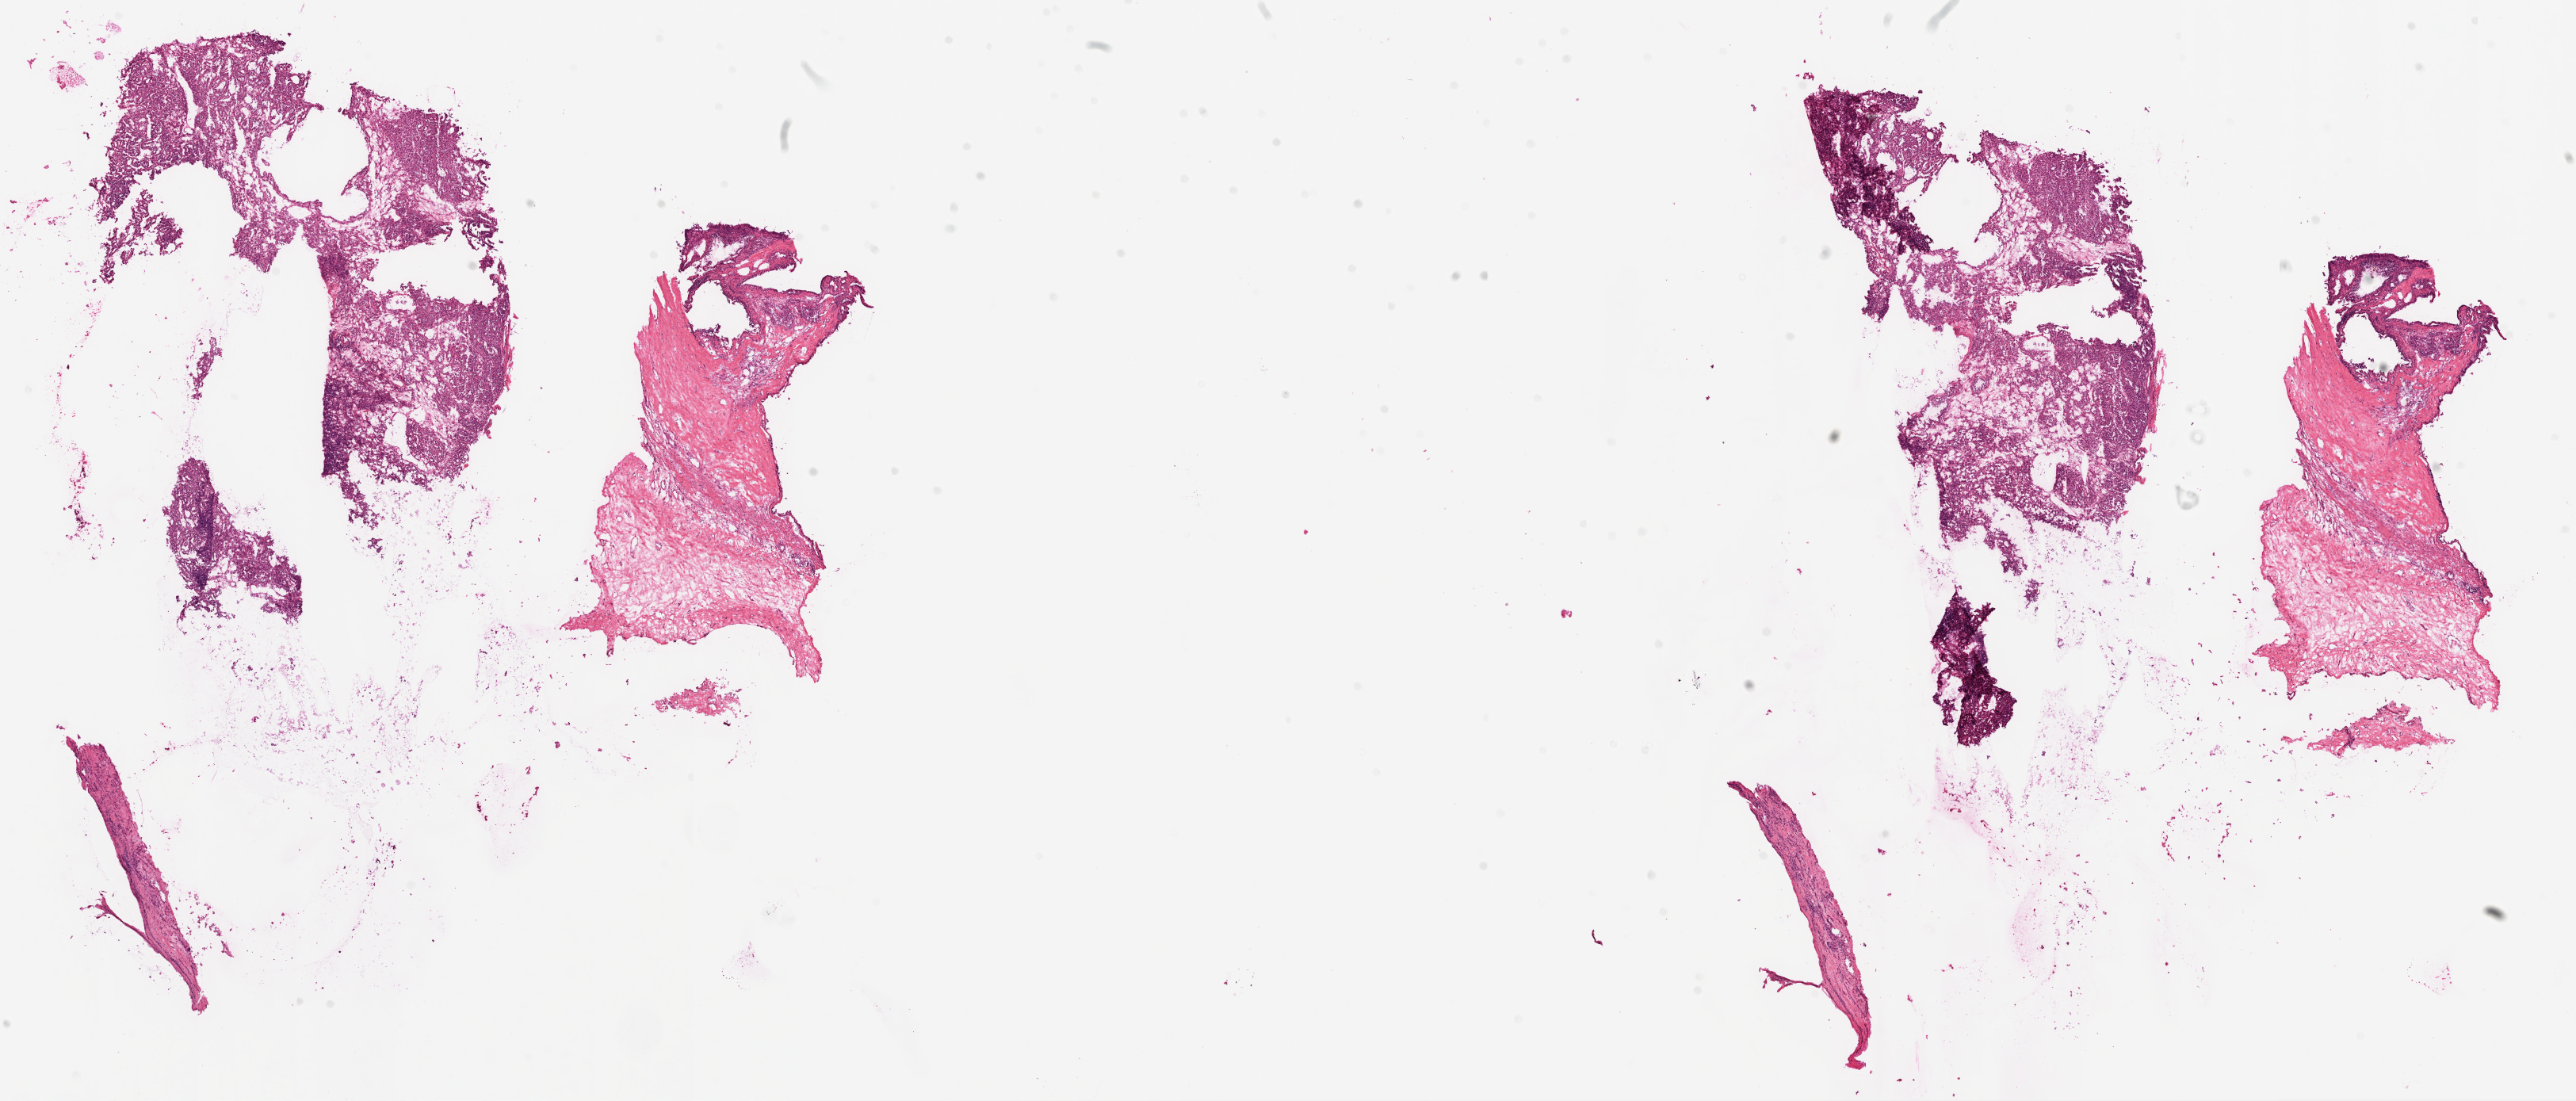
Whole-slide histology image, H&E — low-resolution overview of the scanned area, about 26.1 x 11.1 mm; frozen section from the top of the tissue portion; sample: primary tumour, kidney. Female, age 55 years at initial diagnosis. Histologic grade: G2 (moderately differentiated). Pathologist review of this section (percent, as recorded): tumour cells 60%, tumour nuclei 80%, normal cells 0%, stromal cells 40%, necrosis 0%.
Diagnosis: Clear cell adenocarcinoma, NOS. TNM: T1a NX M0. AJCC pathologic stage: I.